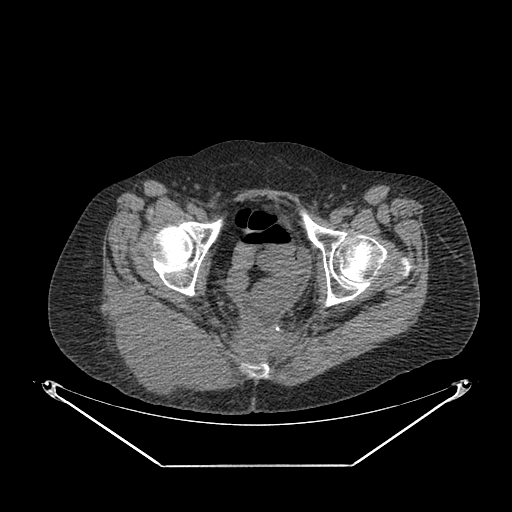
CT of an extremity soft-tissue mass (from a PET/CT study), one axial slice; slice 55 of 267 in the series (ordered by position); reconstruction kernel SOFT; 140 kVp; soft-tissue window (W 400 / L 40 HU); 3.75 mm slice thickness; 512 × 512 image matrix, field of view 500 × 500 mm. Female patient. From the clinical record (not read from this slice): histological type: spindle cell suggestive of myxofibrosarcoma; grade: intermediate; site of the primary tumour: right buttock.
Annotated regions visible in this slice (expert contour drawn on MRI and transferred to this co-registered scan by the dataset authors):
- gross tumour volume (mass): bounding box (x1, y1, x2, y2) in pixels: (109, 299, 216, 398)